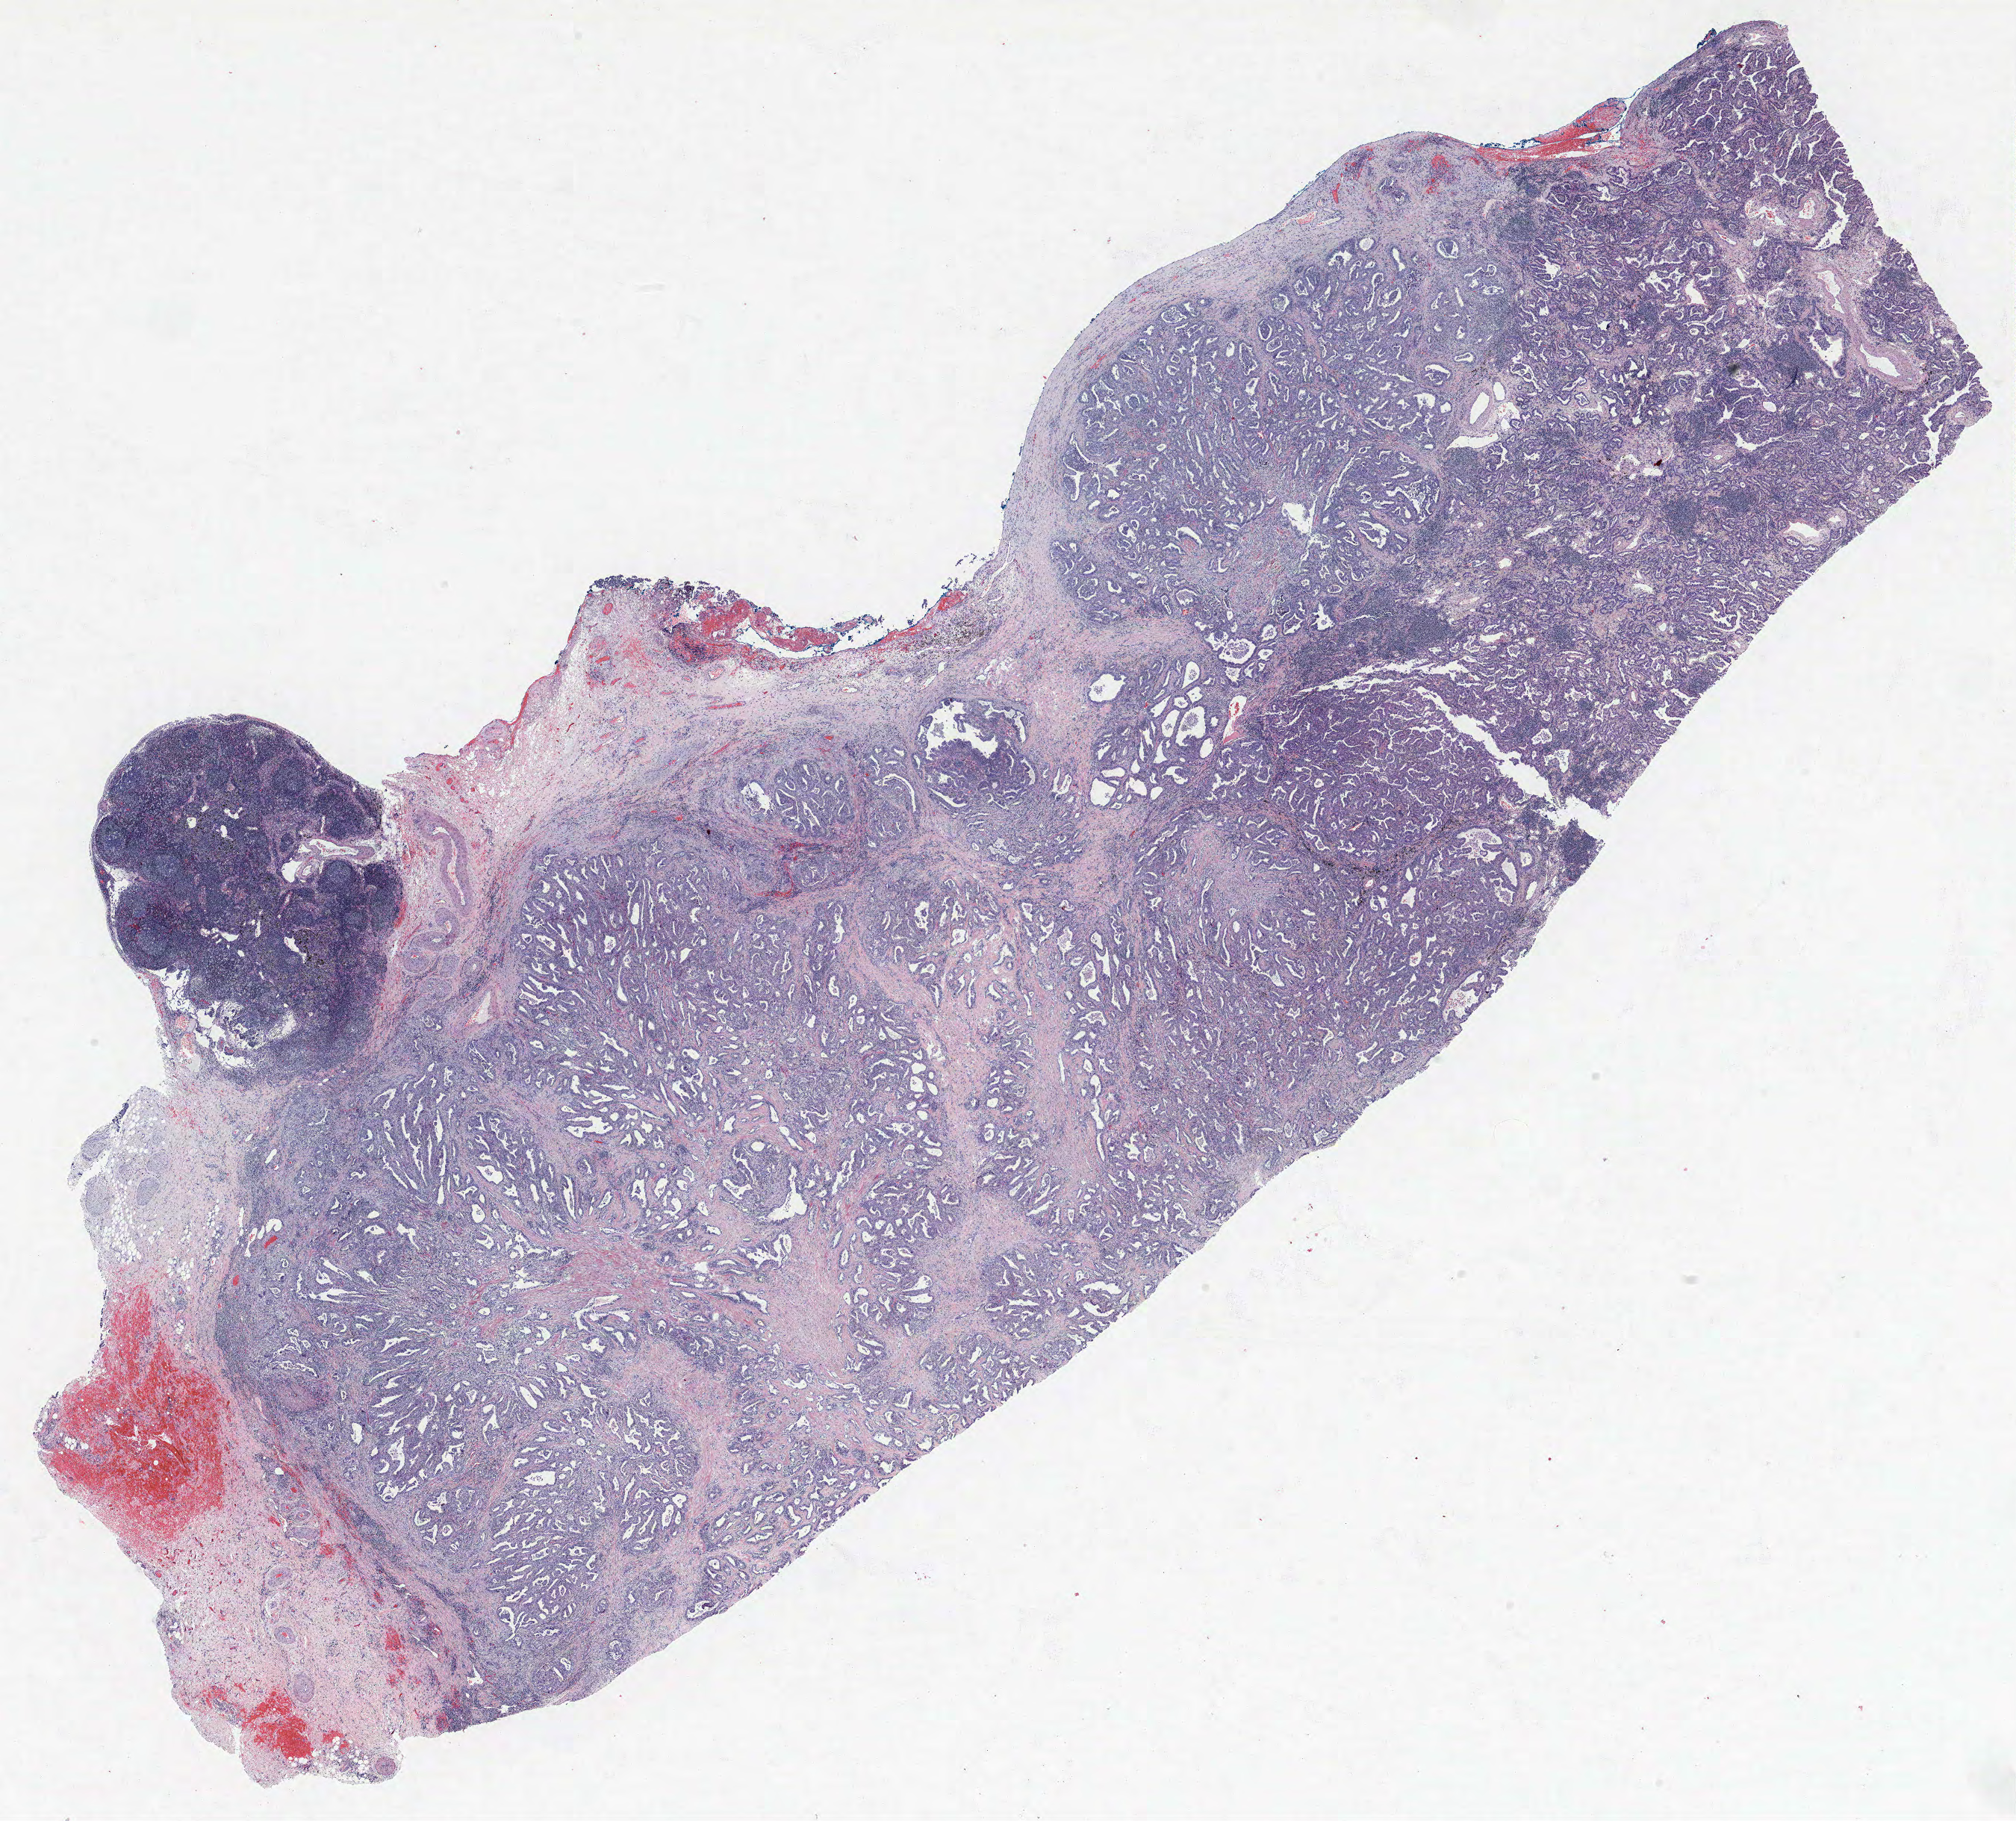
H&E-stained whole-slide image, shown as a low-resolution overview of the whole scanned area (about 21.6 x 19.5 mm, acquisition: 40x scan), formalin-fixed paraffin-embedded (FFPE) section, lung tissue. Female patient, aged 68 at enrolment. Former smoker at enrolment.
Participant's lung-cancer diagnosis: Adenocarcinoma, NOS (ICD-O-3 8140/3).